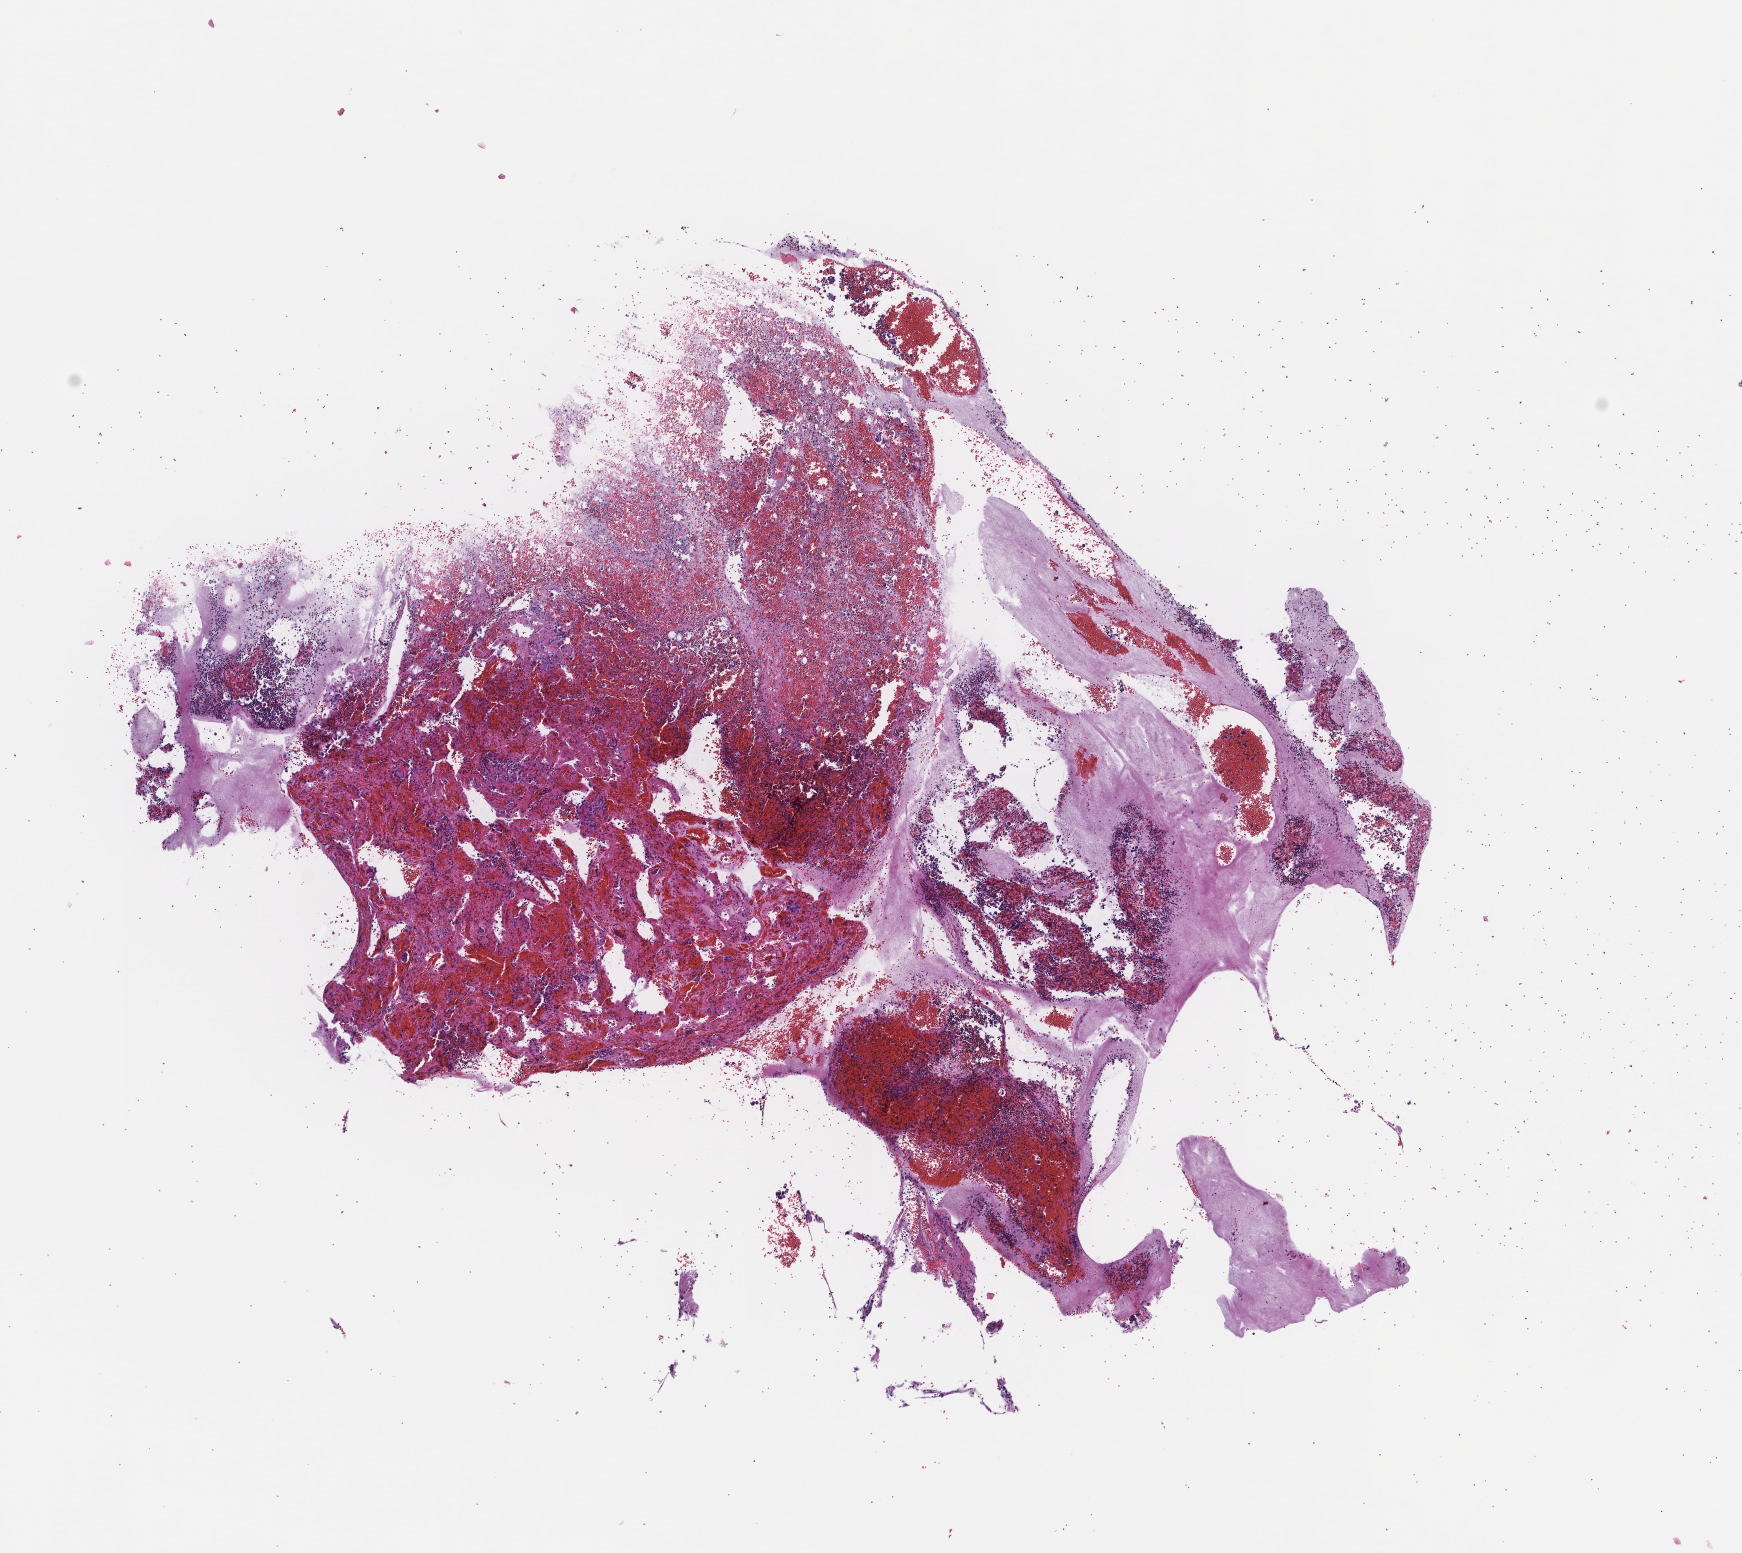
Whole-slide image, H&E stain — low-resolution overview of the scanned area, about 7.0 x 6.3 mm; formalin-fixed, paraffin-embedded (FFPE) tissue; tissue site: lung; archival tissue. Patient: female.
This section: primary tumour tissue. Diagnosis: Non-Small Cell Lung Carcinoma.